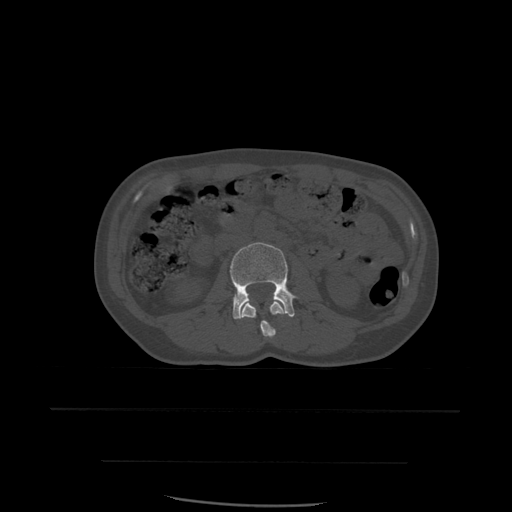
CT including the spine, one axial slice. Slice 207 of 574 in the series (ordered by position). Bone window (W 1800 / L 400 HU). 1.25 mm slice thickness. 512 × 512 image matrix, field of view 392 × 392 mm. Patient age 48 years. Case-level facts recorded for this patient, not image findings: primary cancer: lung; vertebrae with lytic lesions (as recorded): T11.
Annotated regions visible in this slice (semi-automatically segmented with operator editing):
- L2 vertebra: bounding box <240,301,285,339> (left, top, right, bottom; pixels)
- L3 vertebra: <230,242,297,319>